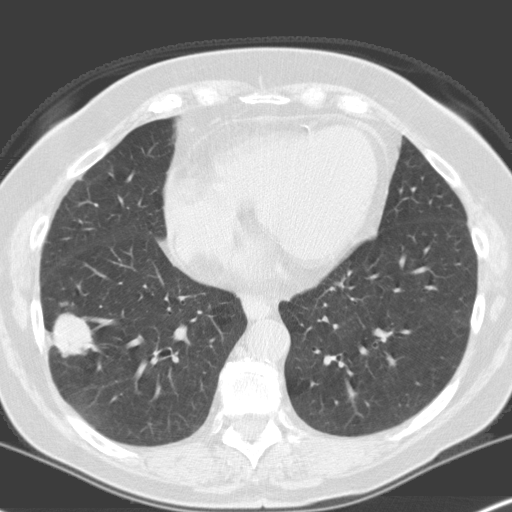
Low-dose screening chest CT, one axial slice. Position 67 of 160 along the scan axis. Lung window (W 1500 / L -600 HU). 3.2 mm slice thickness. 512 × 512 image matrix, field of view 316 × 316 mm.
Annotated regions visible in this slice (expert manual segmentation):
- lesion 1 (tumor, lower lobe of right lung): bounding box <49,313,95,357> (left, top, right, bottom; pixels)